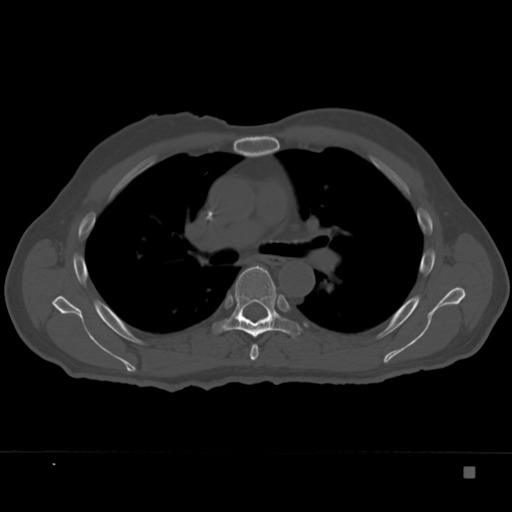
CT including the spine, one axial slice; position 243 of 332 along the scan axis; 120 kVp; bone window (W 1800 / L 400 HU); 512 × 512 image matrix, field of view 389 × 389 mm. Male patient, age 72 years. From the clinical record (not read from this slice): primary cancer: skeletal.
Outlined on this slice (semi-automatically segmented with operator editing):
- T5 vertebra: bounding box (x1, y1, x2, y2) in pixels: (250, 344, 259, 360)
- T6 vertebra: (211, 266, 301, 338)